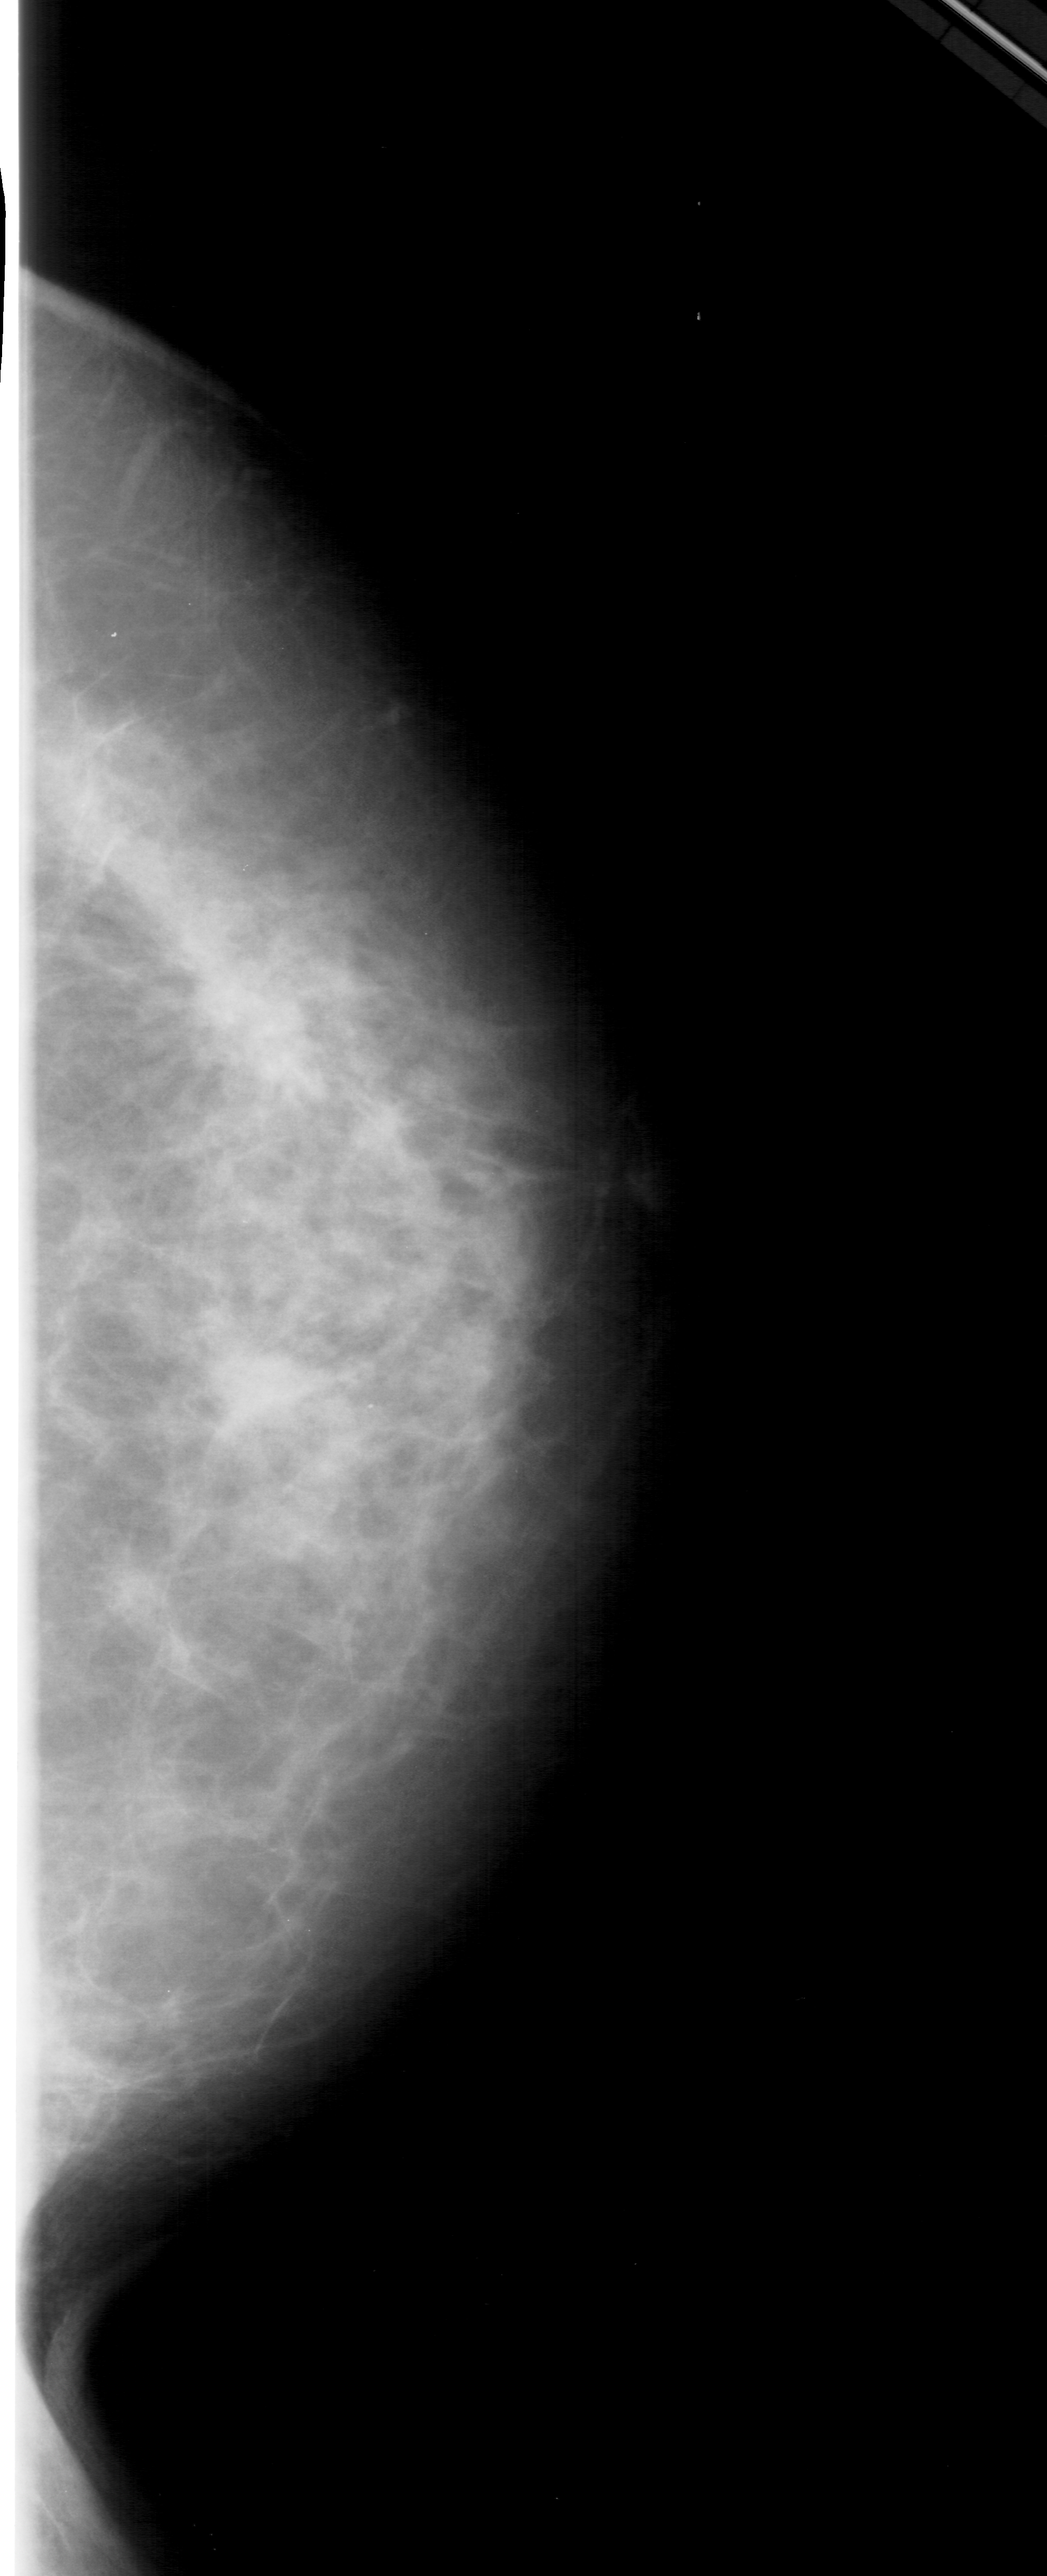
Digitized screen-film mammogram; right breast; craniocaudal (CC) view; BI-RADS breast density category 4 (scale 1–4).
Radiologist-marked abnormalities on this image: mass, shape architectural distortion, margins ill defined; BI-RADS assessment category 4; subtlety rating 1 on a 1 (subtle) to 5 (obvious) scale; pathology (as recorded): benign.